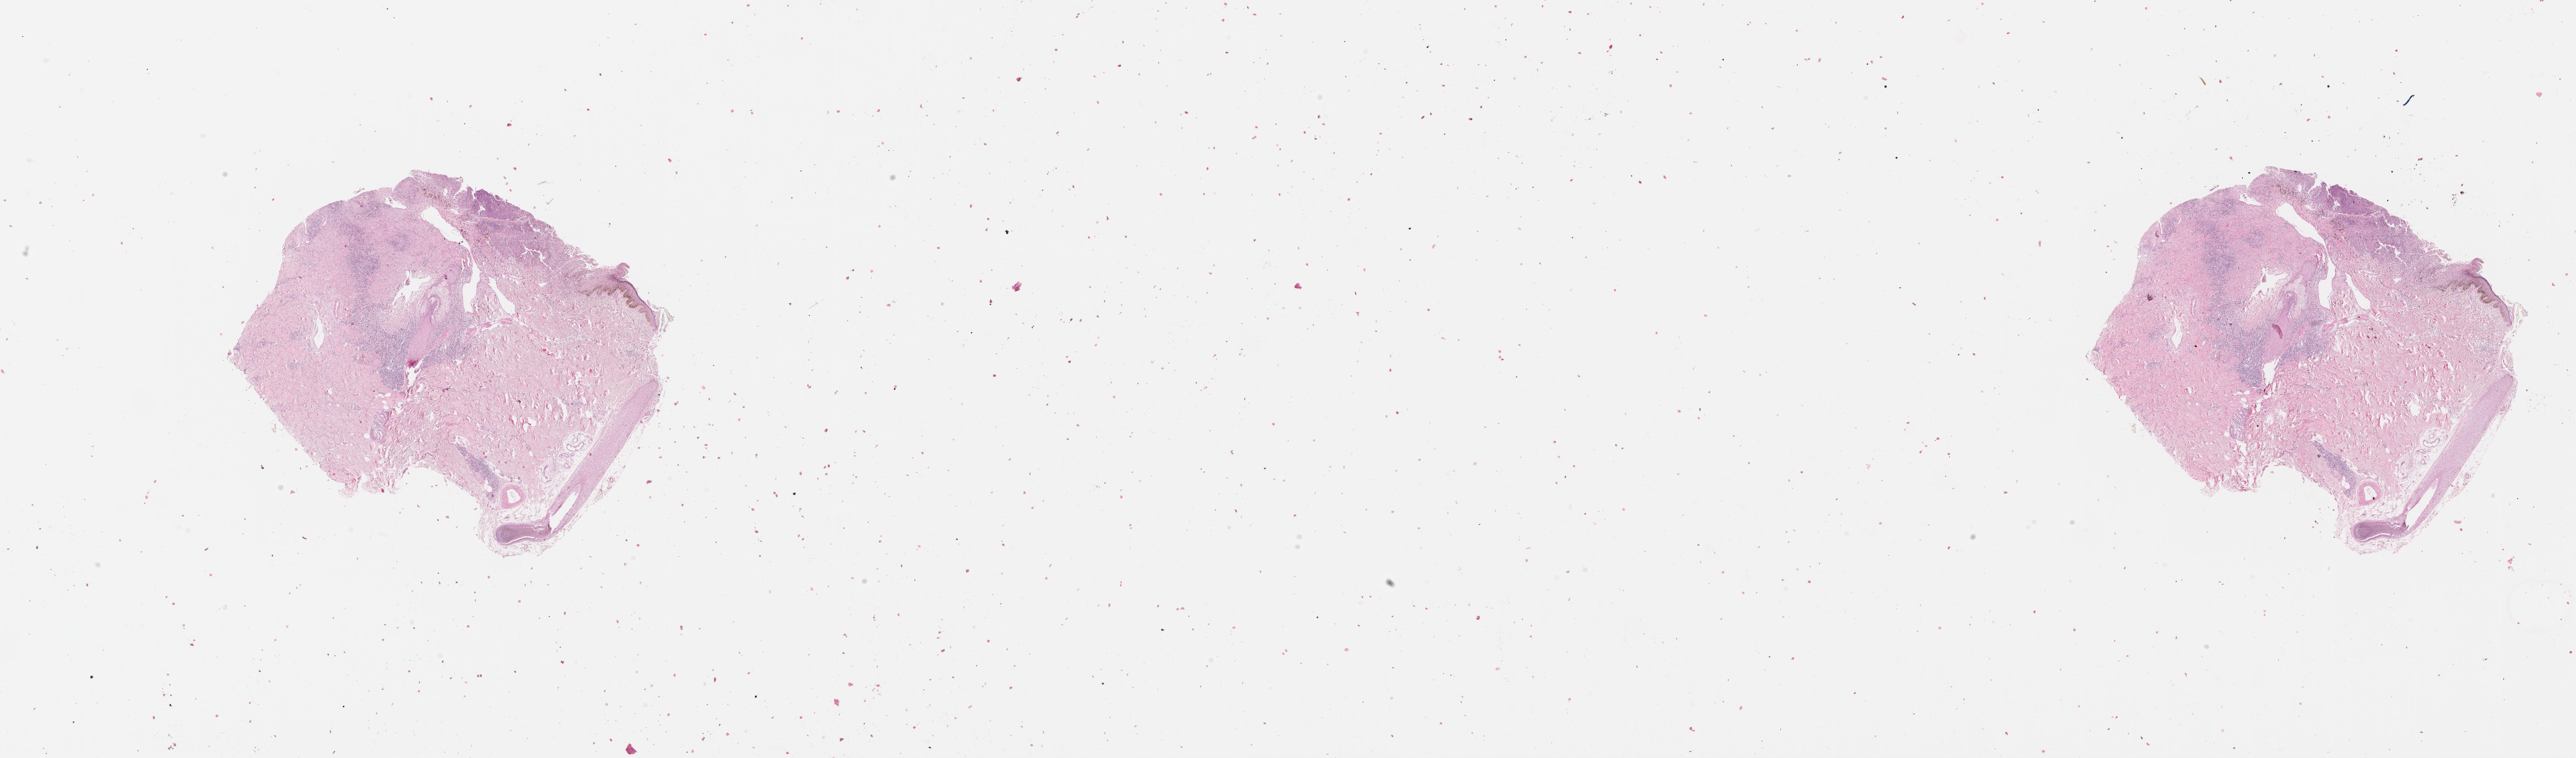
Digitized H&E tissue section (whole slide), low-resolution overview of the scanned area, about 31.1 x 9.1 mm (from a 20x scan). 61-year-old male patient.
- patient diagnosis: Malignant melanoma, NOS